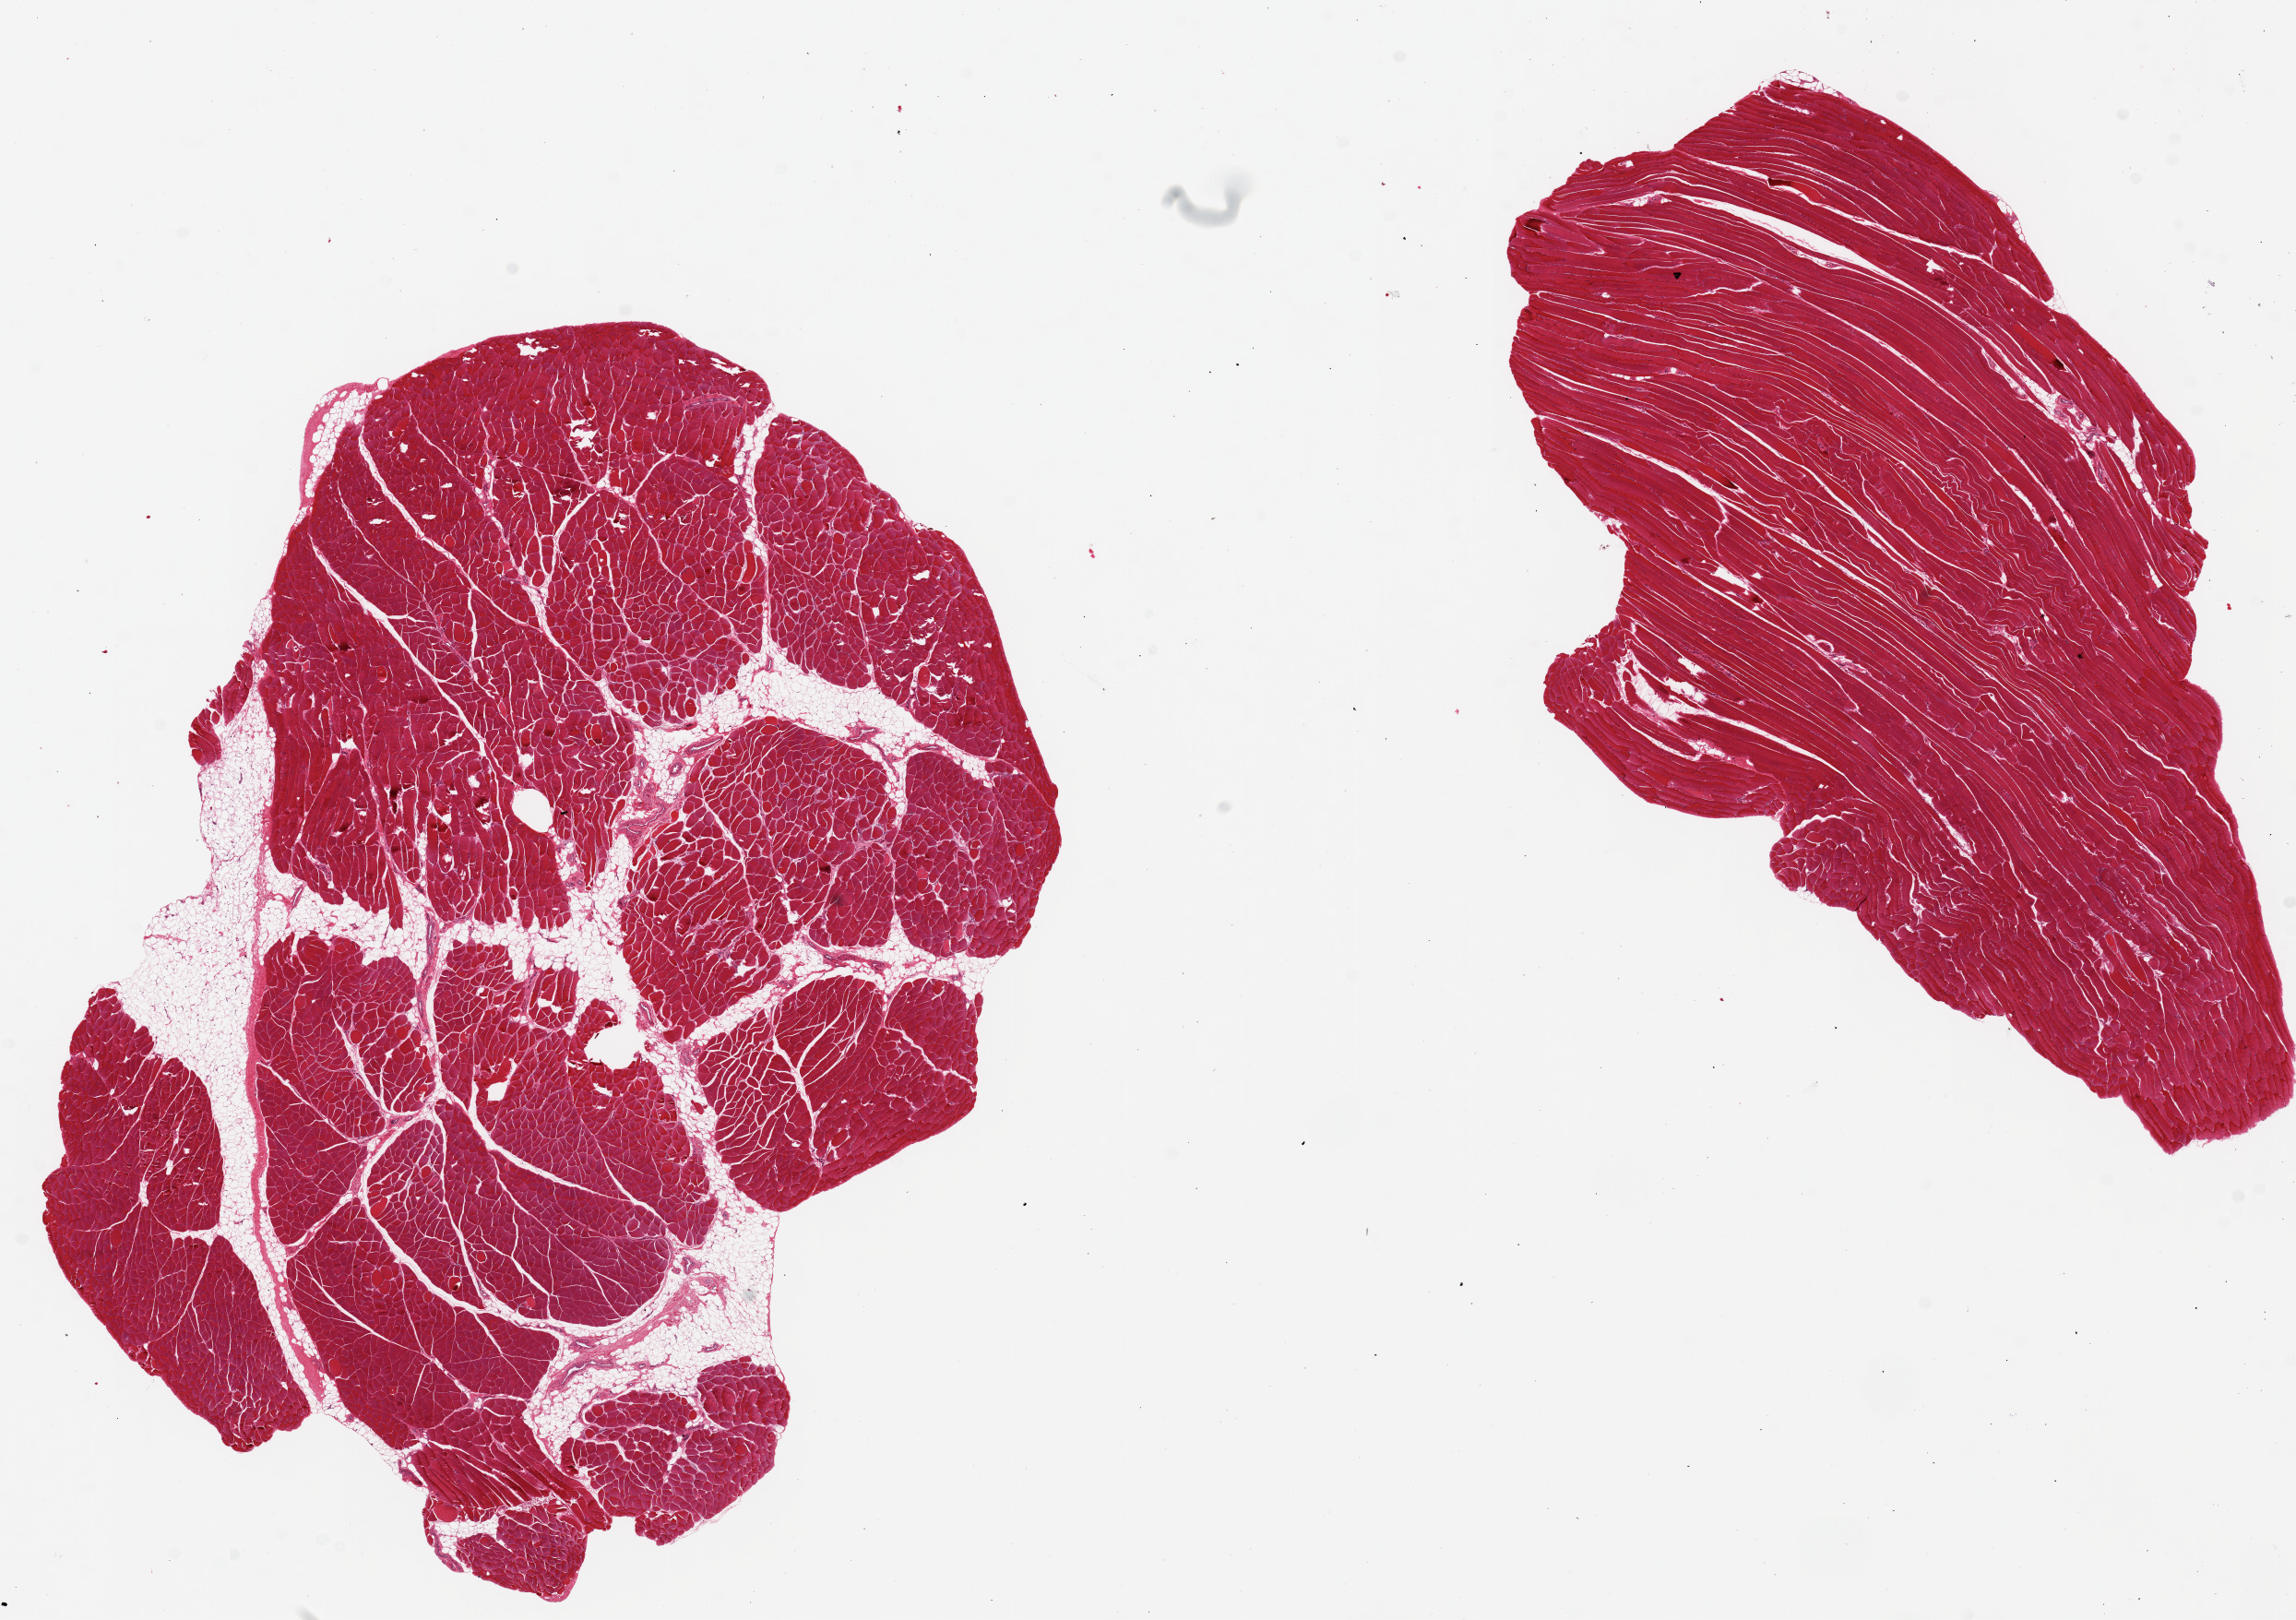
Whole-slide image, hematoxylin and eosin (H&E) stain, whole scanned area (about 19.7 x 13.9 mm) shown as a low-resolution overview, PAXgene-fixed, paraffin-embedded tissue, sampled site (target tissue): skeletal muscle, tissue donor sample. Donor: male.
Review note (as recorded): 2 pieces, 10x8 & 10x7.5mm; ~10% internal adipose in 1 piece.